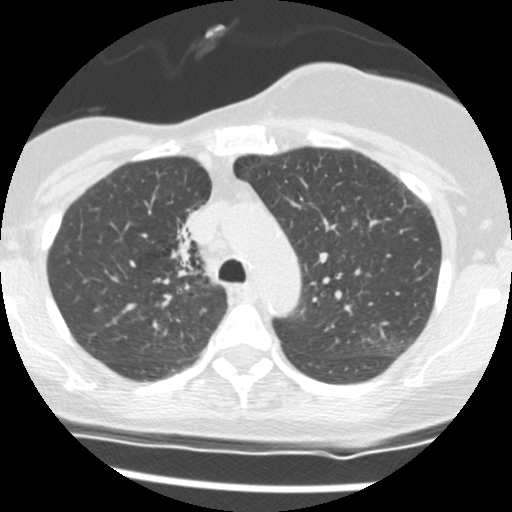
Axial slice from a low-dose chest CT screening exam; second annual screen; lung window (W 1500 / L -600 HU); slice 37 of 165 in the series. Female participant, aged 56 years at enrolment.
Expert reader's lesion annotation, bounding box (x1, y1, x2, y2) in pixels: (154, 202, 213, 279). The screening reader recorded 2 non-calcified nodules or masses ≥4 mm on this exam (right middle lobe, right lower lobe); which of them this box marks is not recorded. Participant outcome: lung cancer diagnosed 675 days after this screen (after the third annual screen) — adenocarcinoma, NOS, right upper lobe, stage IIIB (AJCC 6th edition), 8 mm at pathology.